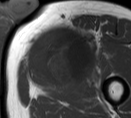
MRI of an extremity soft-tissue mass, one axial slice; position 47 of 55 along the scan axis; MR volume resampled by the dataset authors to the PET/CT grid (not the native acquisition matrix); 3.27 mm slice thickness; 131 × 118 image matrix. Male patient. Case-level facts recorded for this patient, not image findings: histological type: pleiomorphic liposarcoma; grade: high; site of the primary tumour: left thigh.
Structures marked on this image (expert contour drawn on MRI and transferred to this co-registered scan by the dataset authors):
- gross tumour volume including surrounding oedema: bounding box [x1, y1, x2, y2] px = [30, 23, 97, 79]
- gross tumour volume (mass): [30, 30, 88, 79]